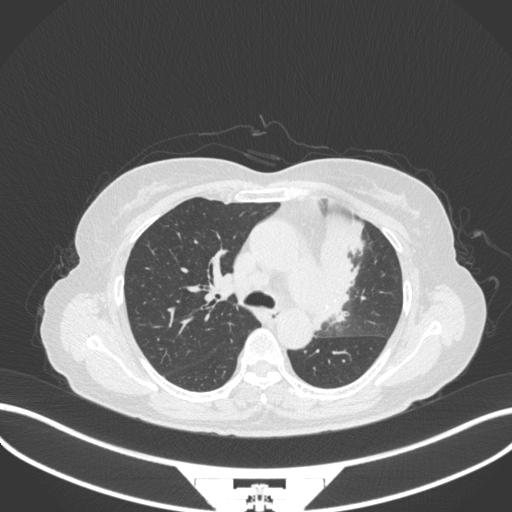
Chest CT, one axial slice; position 221 of 382 along the scan axis; reconstruction kernel B31f; 120 kVp; lung window (W 1500 / L -600 HU); 512 × 512 image matrix. Female patient, age 64 years. Case-level facts recorded for this patient, not image findings: clinical TNM (as recorded): T2a N2 M0.
Outlined on this slice (rectangle marked by the reading radiologist):
- lung tumour (recorded histology: adenocarcinoma): bounding box (x1, y1, x2, y2) in pixels: (311, 203, 367, 332)